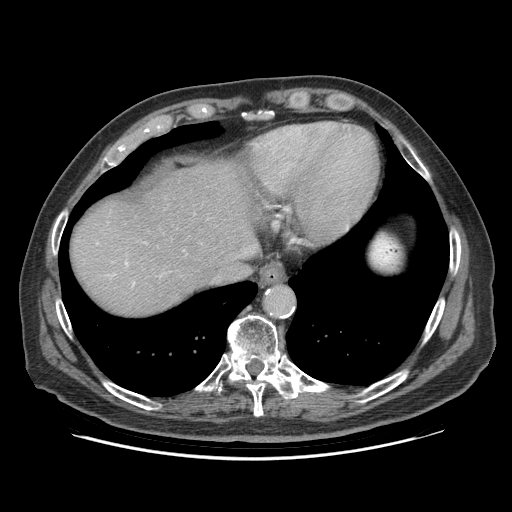
Contrast-enhanced abdominal CT (liver protocol), one axial slice; slice 78 of 95 in the series (ordered by position); reconstruction kernel STANDARD; 140 kVp; soft-tissue window (W 400 / L 40 HU); 2.5 mm slice thickness; 512 × 512 image matrix. From the clinical record (not read from this slice): diagnosis: hepatocellular carcinoma (patient treated with transarterial chemoembolisation; whether this scan precedes or follows treatment is not stated here); TNM stage (as recorded): Stage-IVB; Child-Pugh class: A; tumour differentiation: well differentiated.
Outlined on this slice (semi-automatic segmentation, software-assisted and operator-edited):
- liver parenchyma outside the tumour (the mass and vessels are separate outlines, so this box may not span the whole liver): bounding box [x1, y1, x2, y2] px = [70, 162, 258, 314]
- liver vessels: [125, 262, 128, 265]